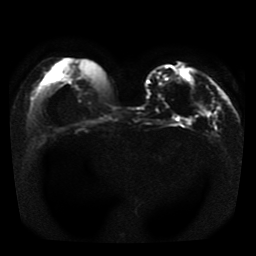
Breast MRI, one axial slice; position 10 of 41 along the scan axis; diffusion-weighted series; image 2 of 4 stored at this slice position (different b-values; order by instance number); 1.5 T; 256 × 256 image matrix, field of view 330 × 330 mm. Female patient.
Annotated regions visible in this slice (outlined manually by an expert reader):
- tumour on diffusion-weighted imaging: bounding box [x1, y1, x2, y2] px = [195, 102, 204, 109]